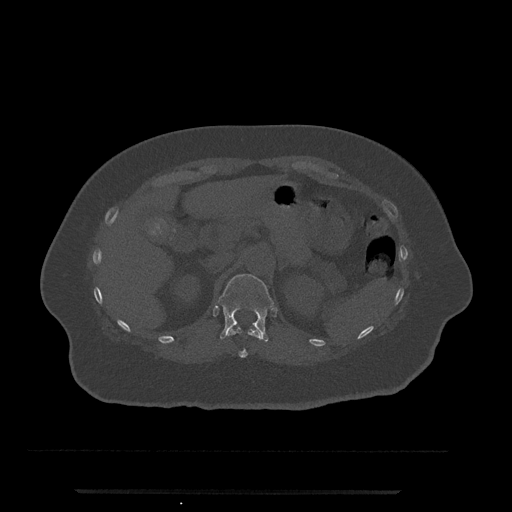
CT including the spine, one axial slice; slice 189 of 797 in the series (ordered by position); reconstruction kernel Br40s/3; 120 kVp; bone window (W 1800 / L 400 HU); 0.5 mm slice thickness; 512 × 512 image matrix, field of view 440 × 440 mm. Female patient, age 51 years. From the clinical record (not read from this slice): primary cancer: neuro.
Annotated regions visible in this slice (semi-automatic segmentation, software-assisted and operator-edited):
- T11 vertebra: bounding box <227,327,261,358> (left, top, right, bottom; pixels)
- T12 vertebra: <218,274,274,342>